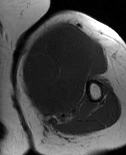
MRI of an extremity soft-tissue mass, one axial slice. Position 48 of 86 along the scan axis. MR volume resampled by the dataset authors to the PET/CT grid (not the native acquisition matrix). 3.27 mm slice thickness. 126 × 155 image matrix, field of view 123 × 151 mm. Female patient. Case-level facts recorded for this patient, not image findings: histological type: pleiomorphic leiomyosarcoma; grade: high; site of the primary tumour: left biceps.
Outlined on this slice (expert contour drawn on MRI and transferred to this co-registered scan by the dataset authors):
- gross tumour volume including surrounding oedema: bounding box (x1, y1, x2, y2) in pixels: (20, 24, 101, 121)
- gross tumour volume (mass): (22, 24, 94, 114)